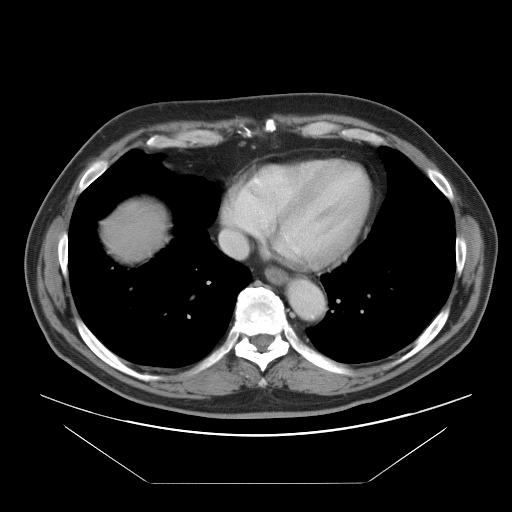
Contrast-enhanced abdominal CT, one axial slice; position 90 of 97 along the scan axis; intravenous contrast given; soft-tissue window (W 400 / L 40 HU); 512 × 512 image matrix. Male patient, age 62 years. Case-level facts recorded for this patient, not image findings: diagnosis: colorectal cancer liver metastases, imaged before liver resection; multiple liver metastases: no; largest metastasis: 7 cm; disease in both lobes: yes.
Annotated regions visible in this slice (outlined manually by an expert reader):
- hepatic veins: box from (x=220, y=187) to (x=247, y=259) px
- liver: (x=108, y=208)–(x=166, y=255)
- planned liver remnant (the part of the liver to remain after resection): (x=108, y=209)–(x=165, y=255)